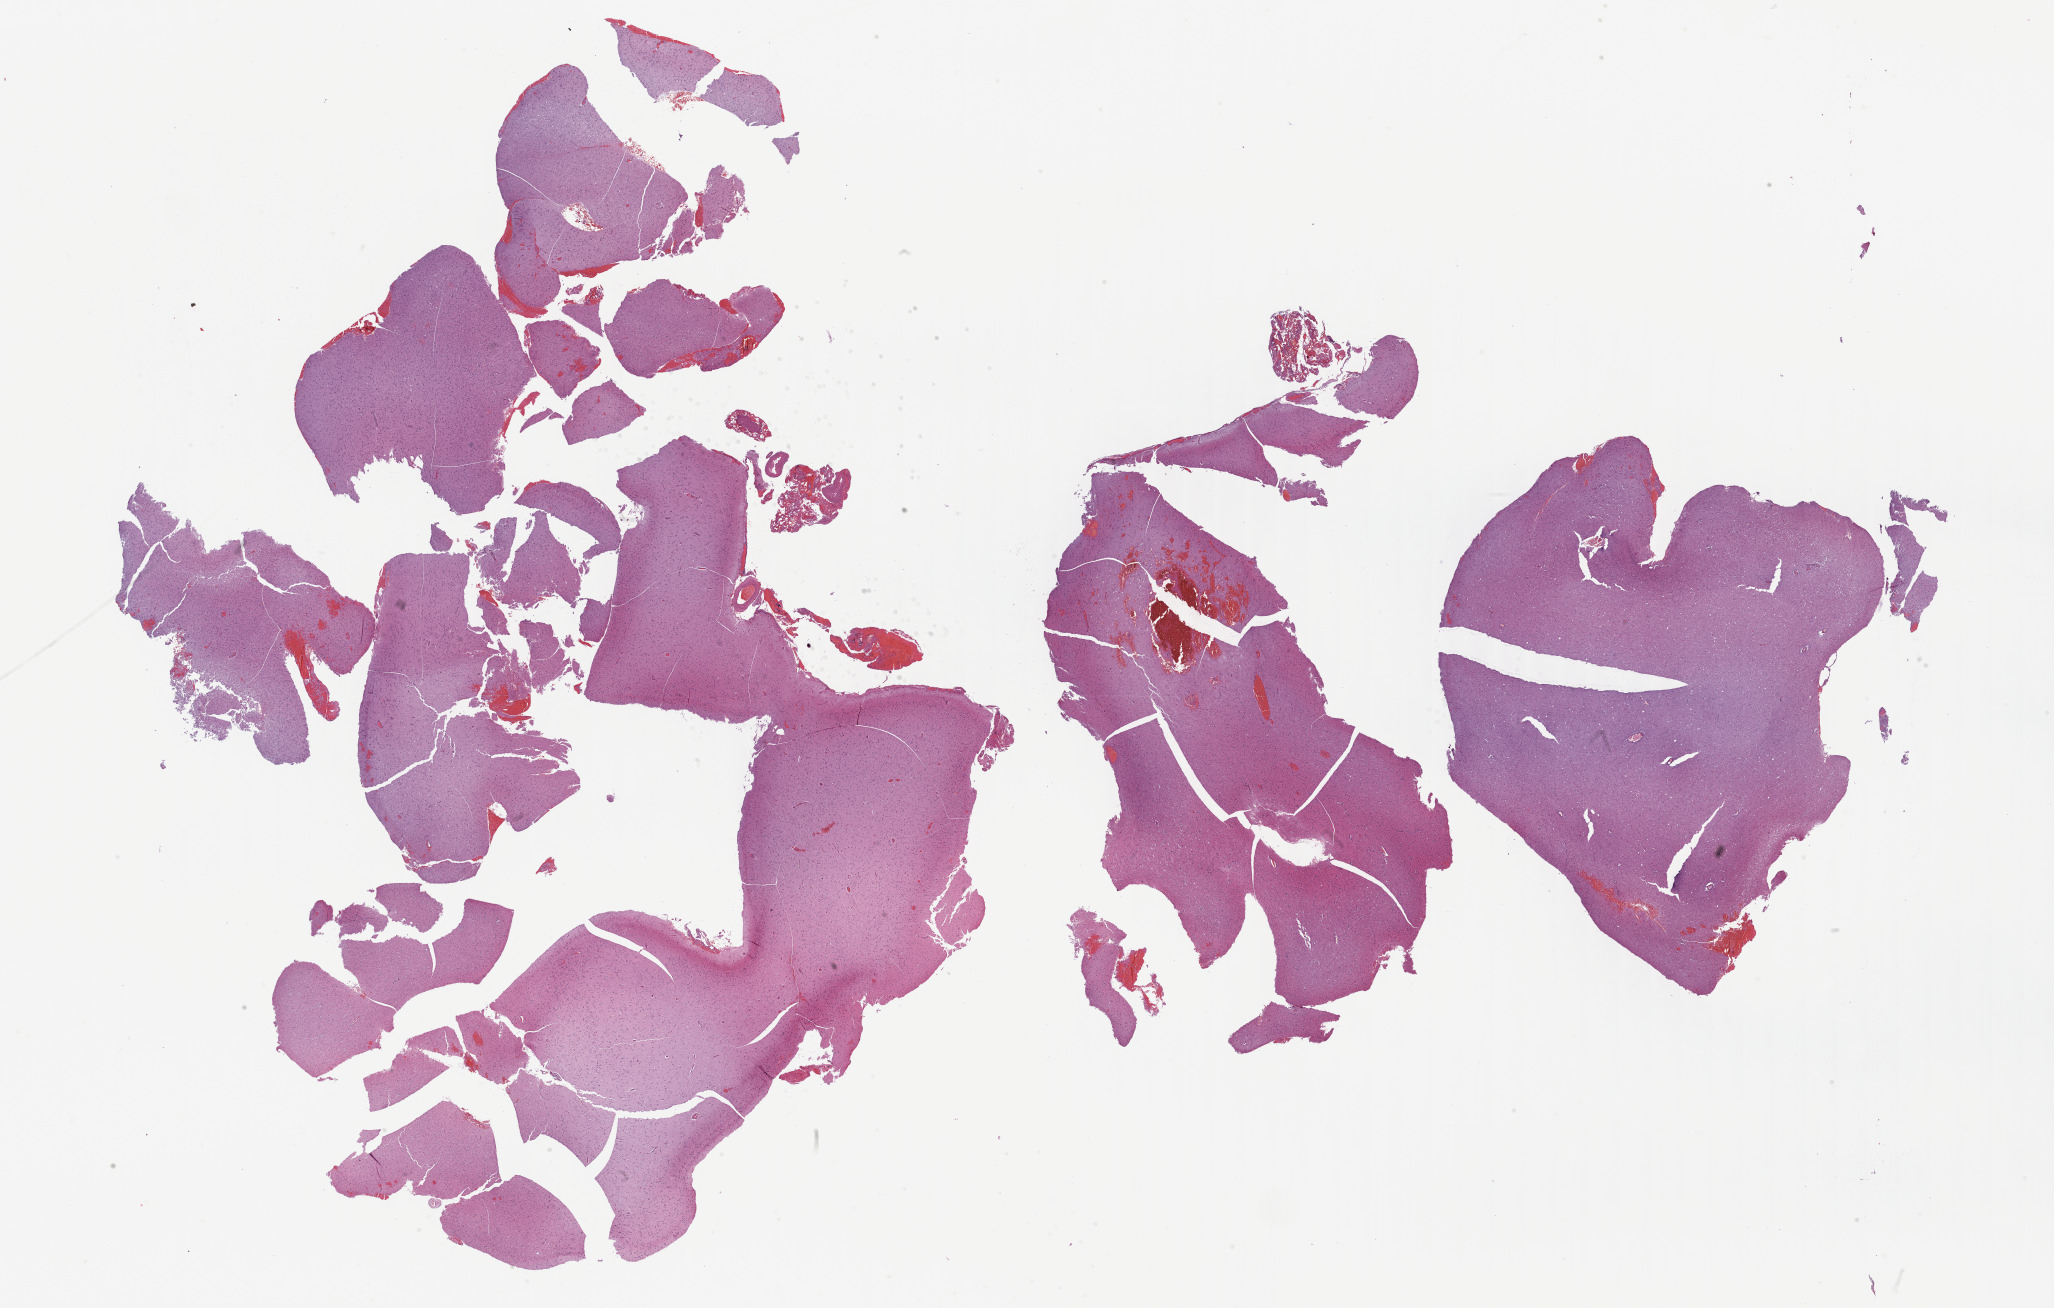
Whole-slide histology image, Hematoxylin and eosin (H&E) stained, shown as a low-resolution overview of the whole scanned area (about 33.2 x 21.2 mm, slide scanned at 40x). Formalin-fixed paraffin-embedded (FFPE) diagnostic section. Brain, primary tumour sample. Patient: male, age at initial diagnosis 58 years. Histologic grade: G3 (poorly differentiated).
Diagnosis: Astrocytoma, anaplastic. Laterality: right.